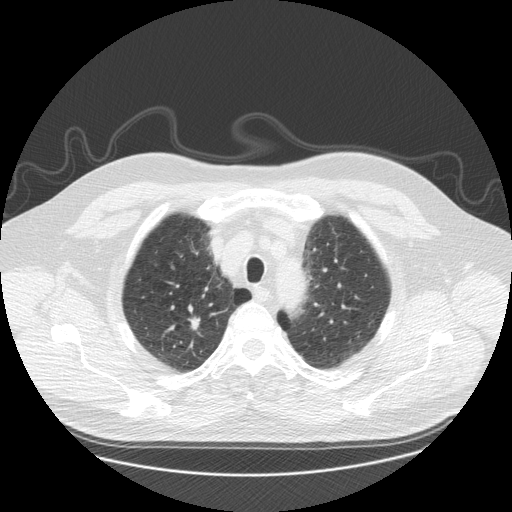
Low-dose screening chest CT, one axial slice. Position 144 of 173 along the scan axis. Reconstruction kernel STANDARD. Lung window (W 1500 / L -600 HU). 2.5 mm slice thickness. 512 × 512 image matrix.
Structures marked on this image (manually delineated by an expert):
- lesion 1 (tumor, upper lobe of right lung): bounding box <188,318,200,330> (left, top, right, bottom; pixels)